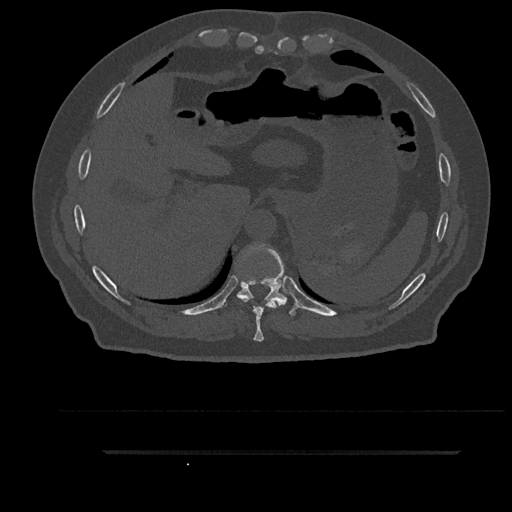
CT including the spine, one axial slice. Position 392 of 797 along the scan axis. Reconstruction kernel Br40s/3. 120 kVp. Bone window (W 1800 / L 400 HU). 512 × 512 image matrix, field of view 432 × 432 mm. Male patient, age 63 years. From the clinical record (not read from this slice): primary cancer: renal.
Structures marked on this image (semi-automatic segmentation, software-assisted and operator-edited):
- T10 vertebra: box from (x=236, y=243) to (x=298, y=316) px
- T9 vertebra: (x=239, y=279)–(x=279, y=342)